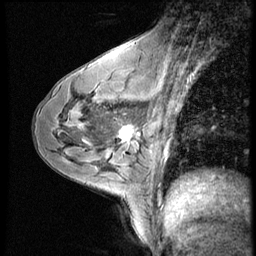
Breast MRI (dynamic contrast-enhanced), one sagittal slice; position 35 of 56 along the scan axis; dynamic contrast-enhanced series, image 2 of 4 at this slice position (ordered by acquisition); 1.5 T; TE 4.2 ms, TR 9 ms; 2.5 mm slice thickness; 256 × 256 image matrix. Patient: female, 43 years. From the clinical record (not read from this slice): setting: breast cancer imaged before/during neoadjuvant chemotherapy; receptor status: HR-positive, HER2-negative.
Outlined on this slice (semi-automatically segmented with operator editing):
- analysis volume of interest (the breast-tissue region the enhancement analysis was run in; not a lesion): bounding box <104,104,152,159> (left, top, right, bottom; pixels)
- tumour enhancement mask (voxels above the 140 % enhancement threshold inside the analysis volume of interest): <121,126,134,143>